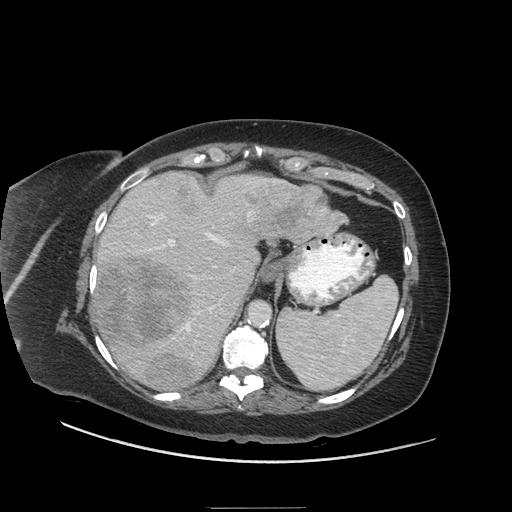
Contrast-enhanced abdominal CT (liver protocol), one axial slice. Position 45 of 81 along the scan axis. Soft-tissue window (W 400 / L 40 HU). 2.5 mm slice thickness. 512 × 512 image matrix. From the clinical record (not read from this slice): diagnosis: hepatocellular carcinoma (patient treated with transarterial chemoembolisation; whether this scan precedes or follows treatment is not stated here); TNM stage (as recorded): Stage-II; Child-Pugh class: A; tumour size: 1.7 cm.
Structures marked on this image (semi-automatically segmented with operator editing):
- liver parenchyma outside the tumour (the mass and vessels are separate outlines, so this box may not span the whole liver): bounding box <90,172,295,388> (left, top, right, bottom; pixels)
- mass: <96,174,345,392>
- liver vessels: <102,179,284,358>